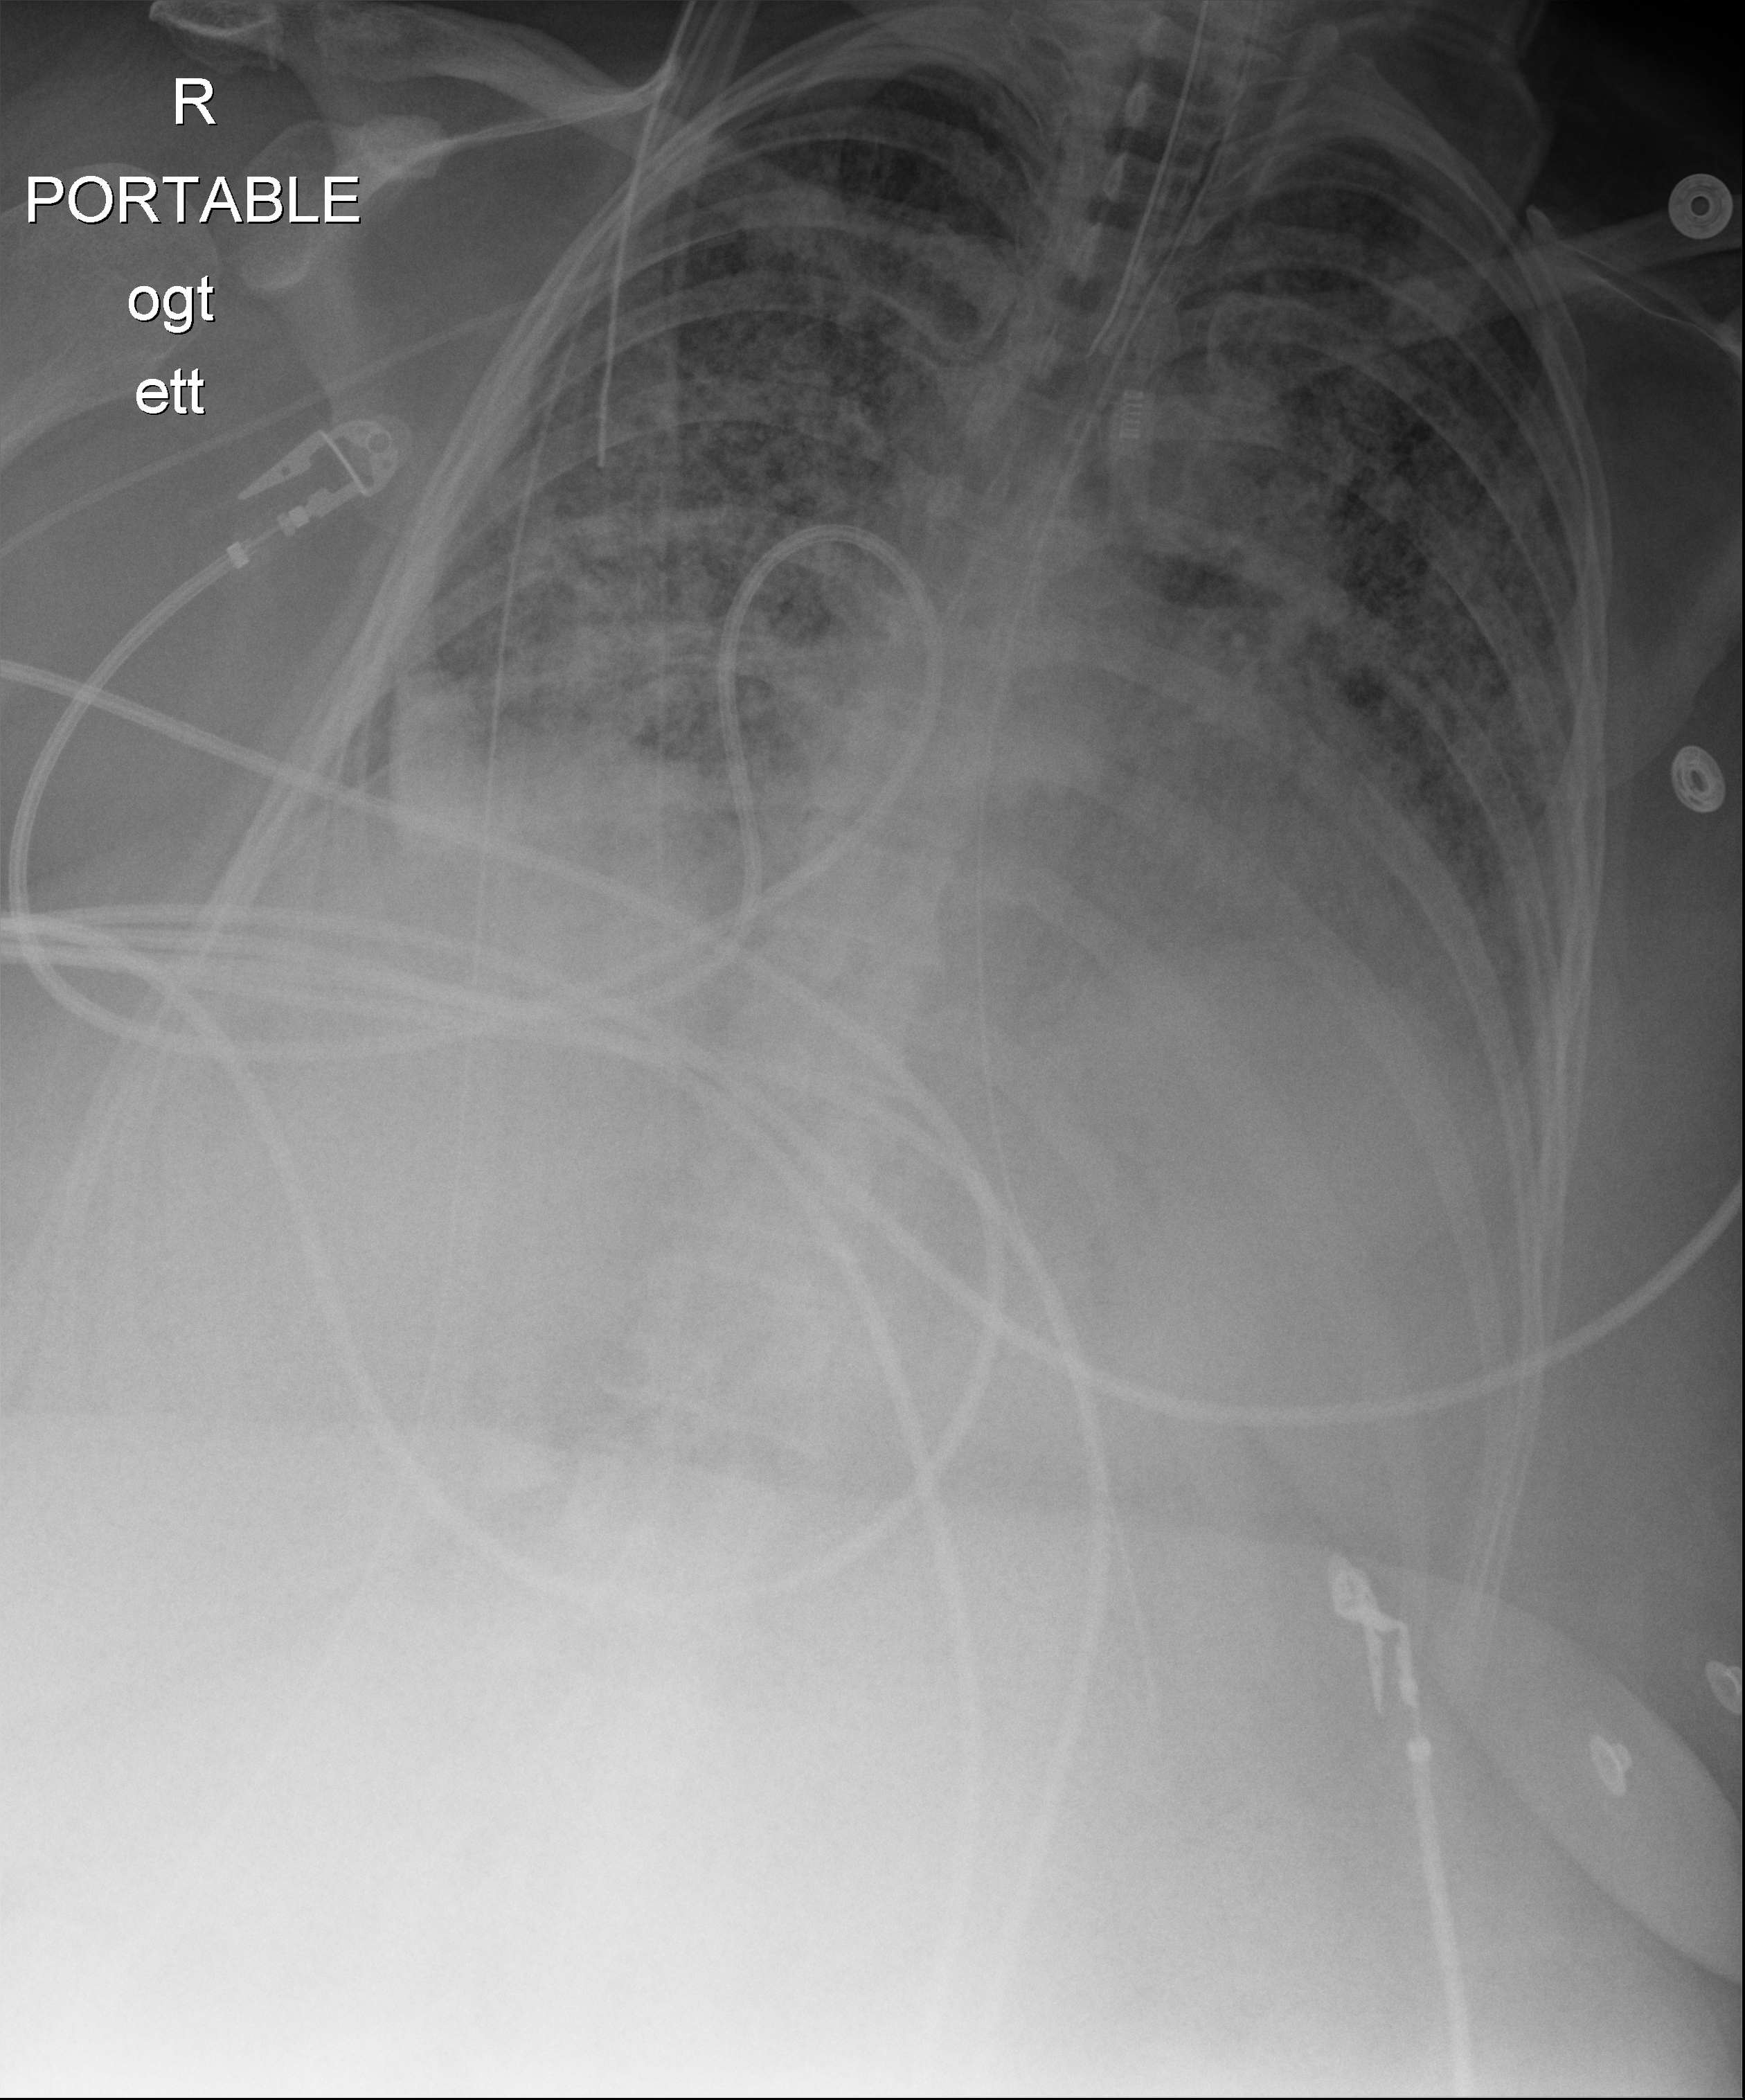
Chest radiograph, anteroposterior (AP) projection. Patient hospitalised with COVID-19; female, aged 18–59 years.
From the hospital-stay record, not from the radiograph (when in the stay this image was taken is not recorded): diabetes (admission record): no; admitted to intensive care during this hospital stay: yes.